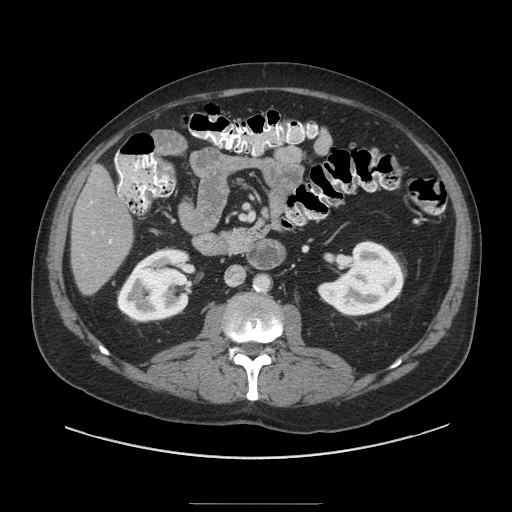
Contrast-enhanced abdominal CT (liver protocol), one axial slice. Position 30 of 91 along the scan axis. Reconstruction kernel STANDARD. 140 kVp. Soft-tissue window (W 400 / L 40 HU). 2.5 mm slice thickness. 512 × 512 image matrix, field of view 440 × 440 mm. From the clinical record (not read from this slice): diagnosis: hepatocellular carcinoma (patient treated with transarterial chemoembolisation; whether this scan precedes or follows treatment is not stated here); TNM stage (as recorded): Stage-I; Child-Pugh class: A.
Structures marked on this image (semi-automatically segmented with operator editing):
- liver parenchyma outside the tumour (the mass and vessels are separate outlines, so this box may not span the whole liver): bounding box [x1, y1, x2, y2] px = [70, 166, 132, 294]
- liver vessels: [90, 195, 121, 244]